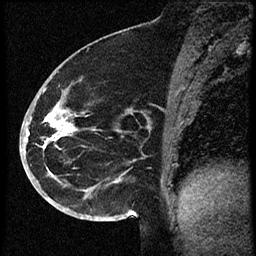
Breast MRI (dynamic contrast-enhanced), one sagittal slice; position 30 of 60 along the scan axis; dynamic contrast-enhanced study with each time point stored as its own series, time point 2 of 3 at this slice position (early post-contrast, ordered by acquisition time); 1.5 T; TE 4.2 ms, TR 18.9 ms; 2 mm slice thickness; 256 × 256 image matrix, field of view 200 × 200 mm. Female patient. From the clinical record (not read from this slice): setting: breast cancer imaged before/during neoadjuvant chemotherapy; receptor status: HR-positive, HER2-negative.
Annotated regions visible in this slice (semi-automatically segmented with operator editing):
- analysis volume of interest (the breast-tissue region the enhancement analysis was run in; not a lesion): bounding box (x1, y1, x2, y2) in pixels: (30, 87, 104, 173)
- tumour enhancement mask (voxels above the 100 % enhancement threshold inside the analysis volume of interest): (44, 108, 75, 149)